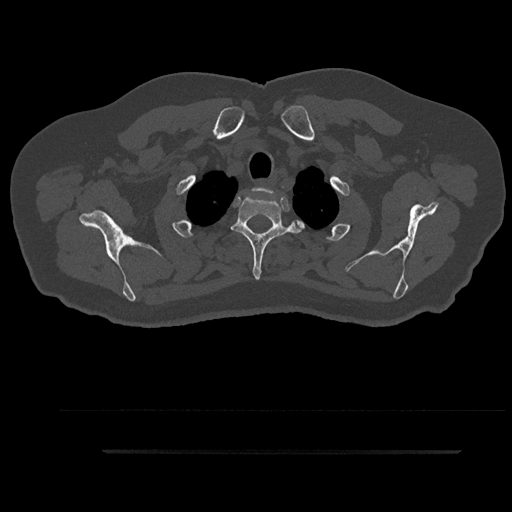
CT including the spine, one axial slice. Position 757 of 797 along the scan axis. Reconstruction kernel Br40s/3. Bone window (W 1800 / L 400 HU). 0.5 mm slice thickness. 512 × 512 image matrix, field of view 432 × 432 mm. Patient: male, 63 years. Case-level facts recorded for this patient, not image findings: primary cancer: renal.
Outlined on this slice (semi-automatic segmentation, software-assisted and operator-edited):
- T1 vertebra: bounding box [x1, y1, x2, y2] px = [254, 188, 284, 208]
- T2 vertebra: [231, 196, 304, 279]
- T3 vertebra: [219, 245, 294, 249]